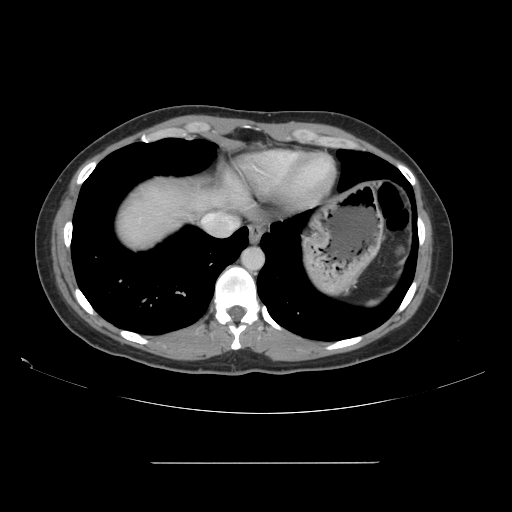
Contrast-enhanced abdominal CT, one axial slice; slice 139 of 151 in the series (ordered by position); soft-tissue window (W 400 / L 40 HU); 2.5 mm slice thickness; 512 × 512 image matrix, field of view 421 × 421 mm. Female patient, age 46 years. Case-level facts recorded for this patient, not image findings: diagnosis: colorectal cancer liver metastases, imaged before liver resection.
Outlined on this slice (outlined manually by an expert reader):
- hepatic veins: box from (x=203, y=214) to (x=216, y=223) px
- liver: (x=121, y=187)–(x=222, y=244)
- planned liver remnant (the part of the liver to remain after resection): (x=136, y=187)–(x=187, y=220)